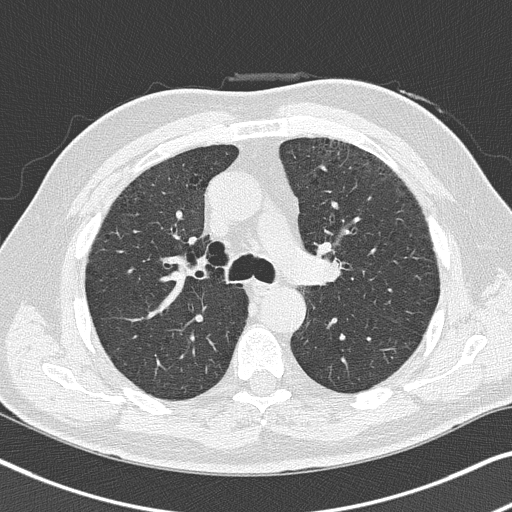
Axial slice from a low-dose chest CT screening exam, baseline screening round, lung window (W 1500 / L -600 HU), lung (sharp) reconstruction kernel (B50f), slice 111 of 300 in the series, 512 × 512 image matrix. Male participant, aged 64 years at enrolment.
Expert reader's lesion annotation, box from (x=322, y=245) to (x=356, y=276) px. Reader record for this screening exam (exam-level; its link to the box is not recorded): non-calcified nodule or mass ≥4 mm, left upper lobe, 4 × 4 mm, smooth margins, soft tissue attenuation. Lung cancer was diagnosed 450 days after this screen: squamous cell carcinoma, keratinizing, NOS, left upper lobe, moderately differentiated (G2), stage IA (AJCC 6th edition), 4 mm at pathology.